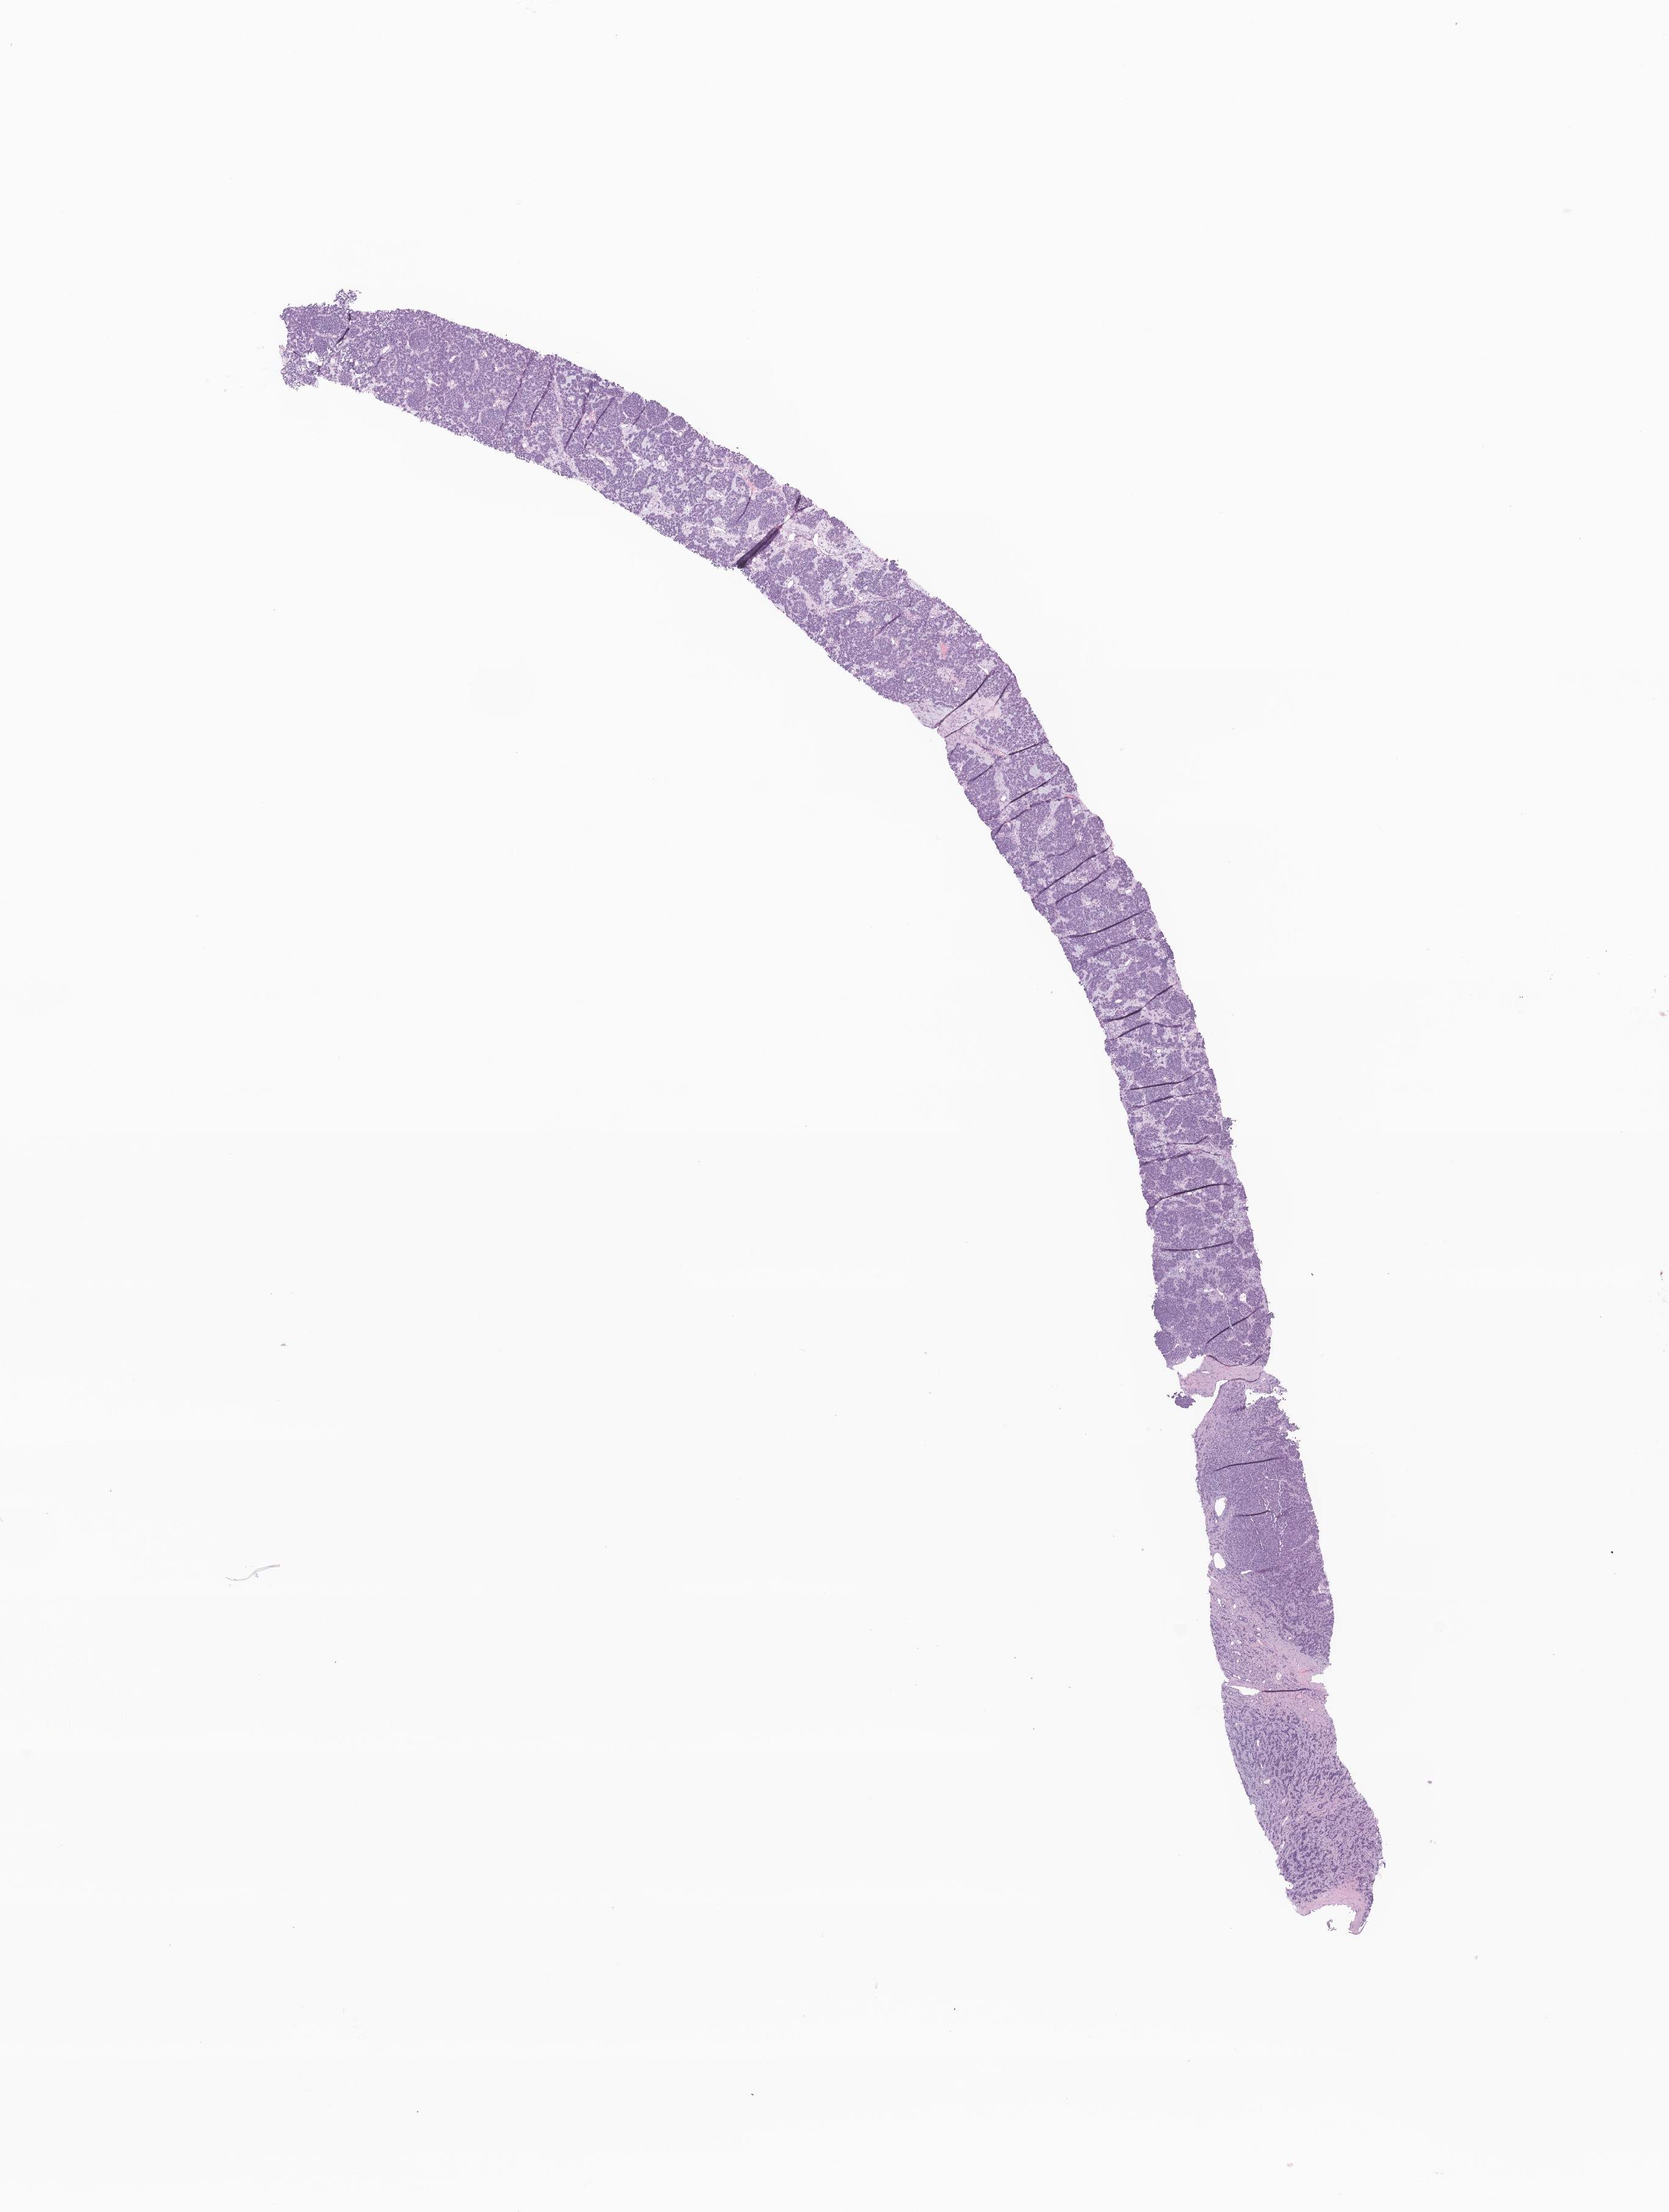
Digitized H&E-stained section of tumor tissue from the skin of scalp and neck, shown as a low-resolution overview of the whole scanned area (about 11.5 x 15.3 mm); FFPE section. Patient female; age 145 months.
* recorded diagnosis: Neuroendocrine carcinoma, NOS